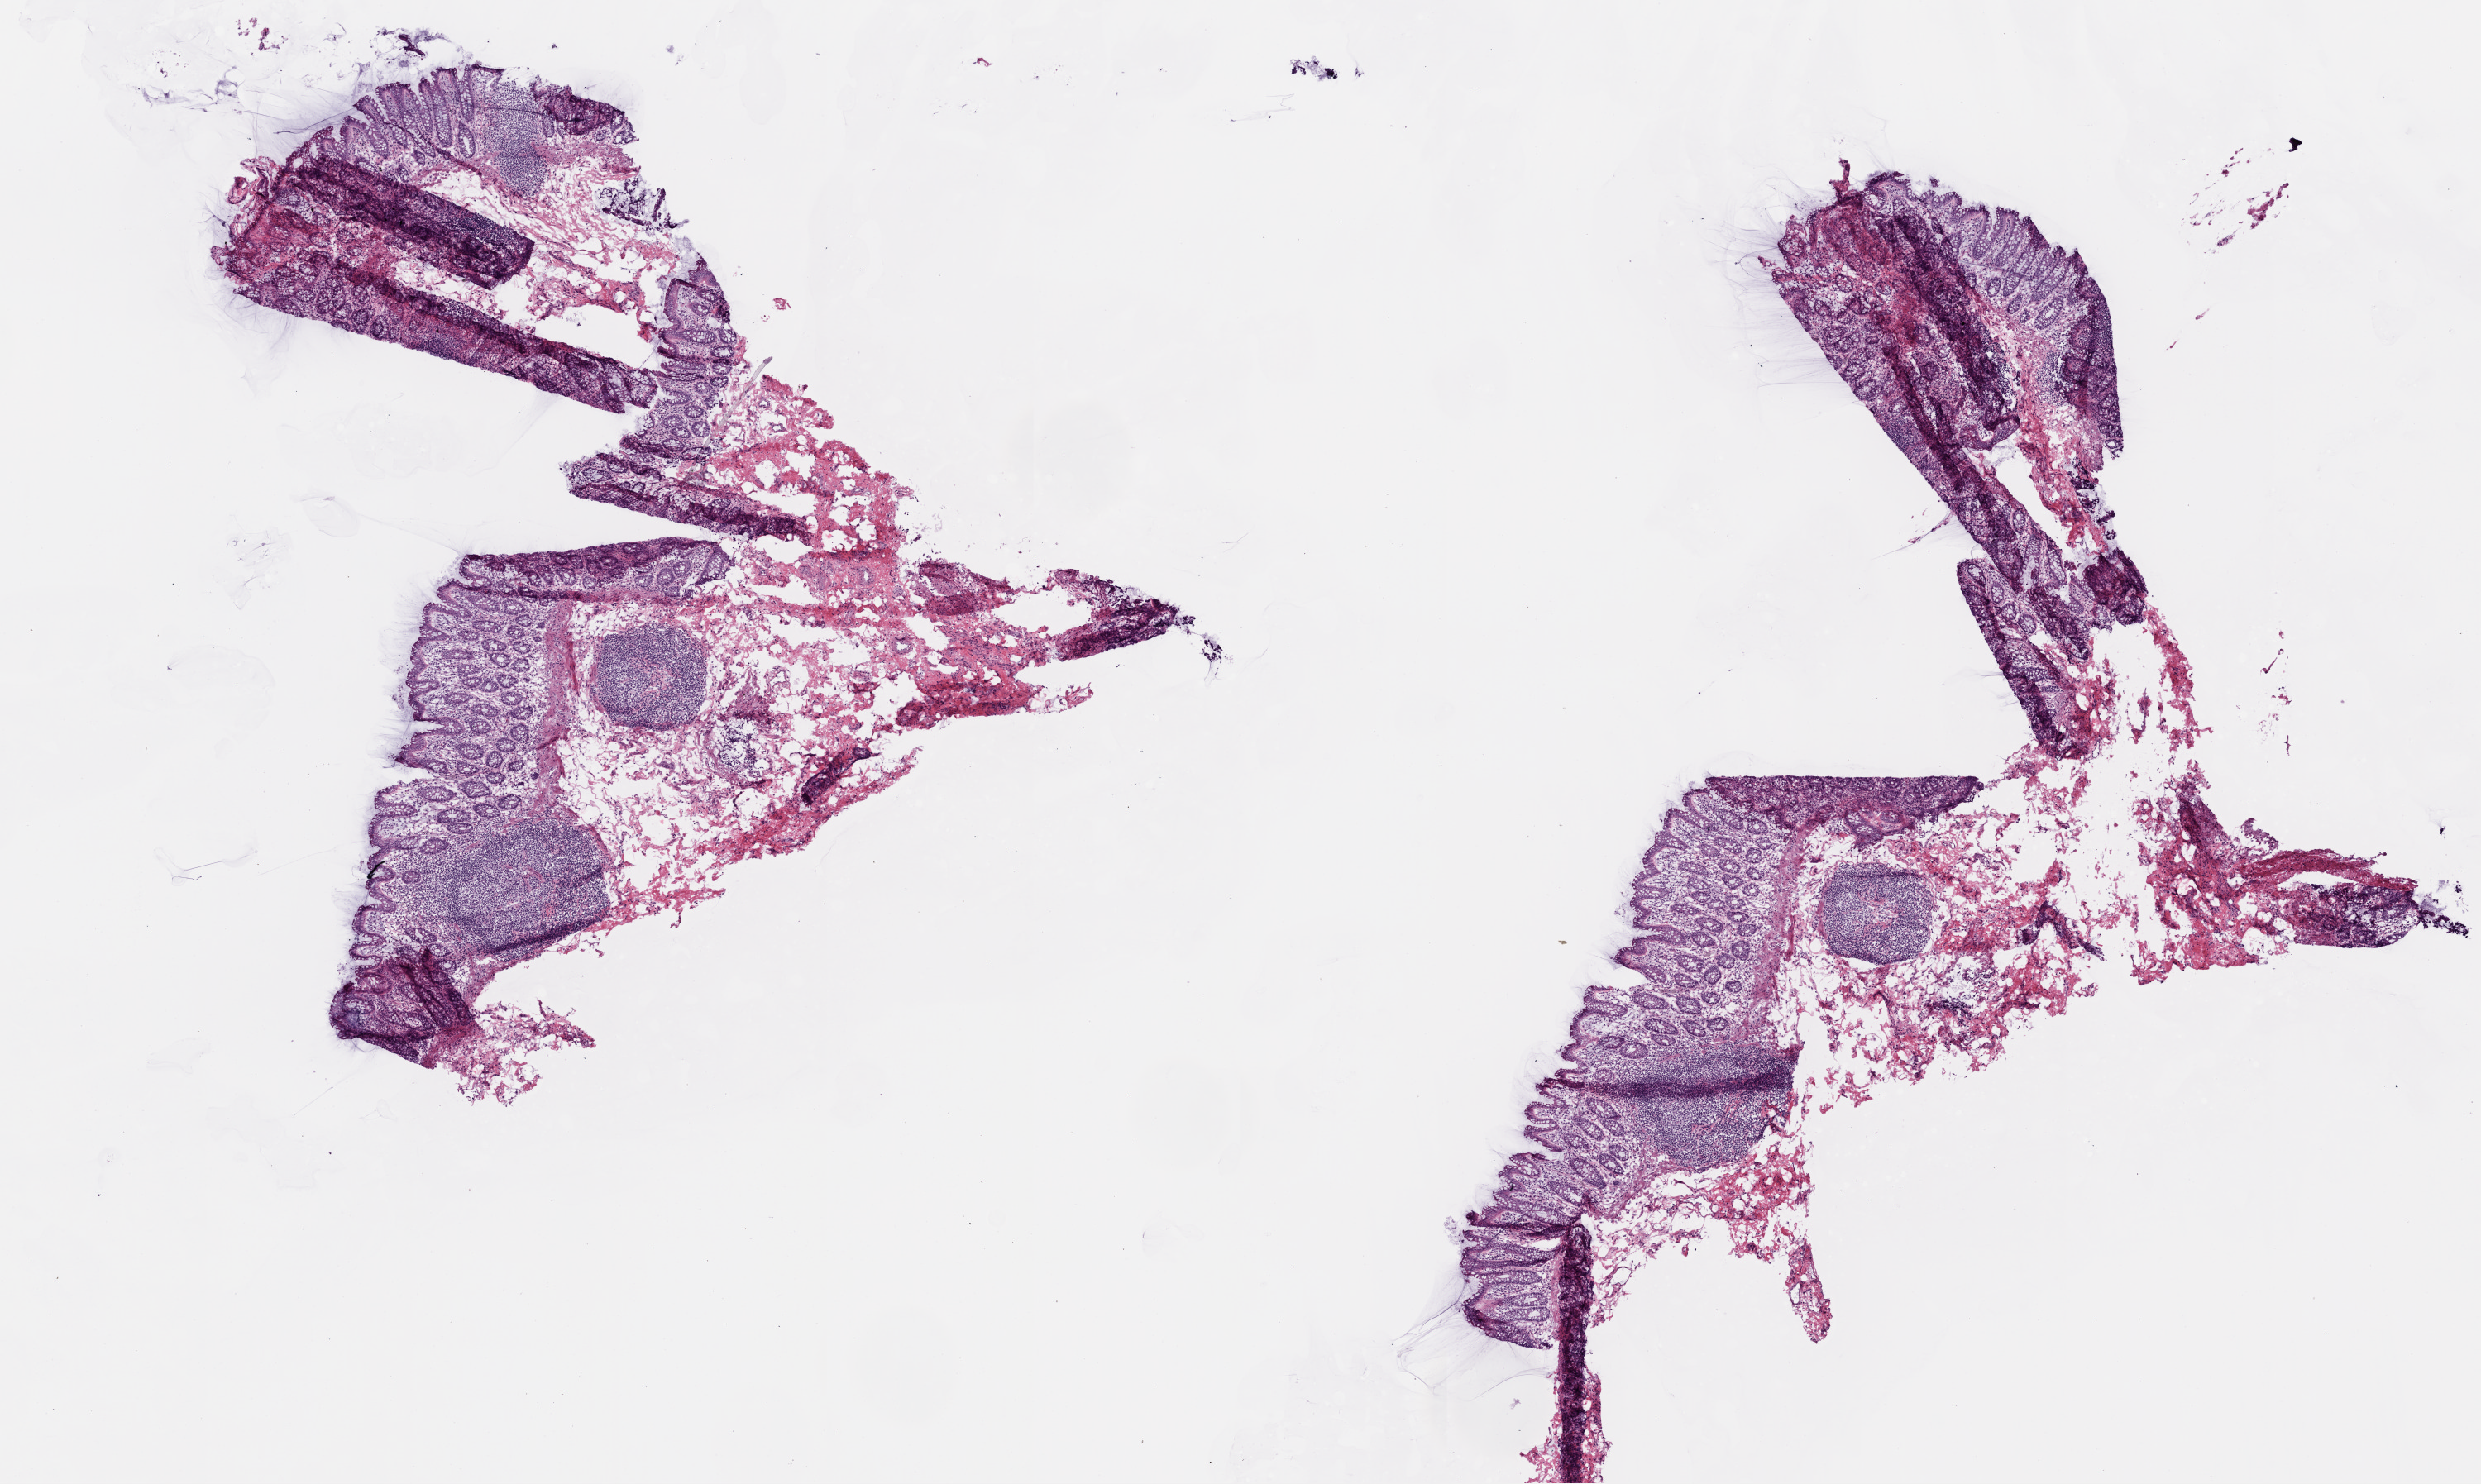
H&E whole-slide image, whole scanned area (about 12.0 x 7.2 mm, acquisition: 20x scan) shown as a low-resolution overview; frozen section from the top of the tissue portion; solid tissue normal (non-tumour tissue) sample from the colon. Female, age 75 years at initial diagnosis.
This section: solid tissue normal sample (biorepository sample class). Patient diagnosis: Adenocarcinoma, NOS (sigmoid colon).